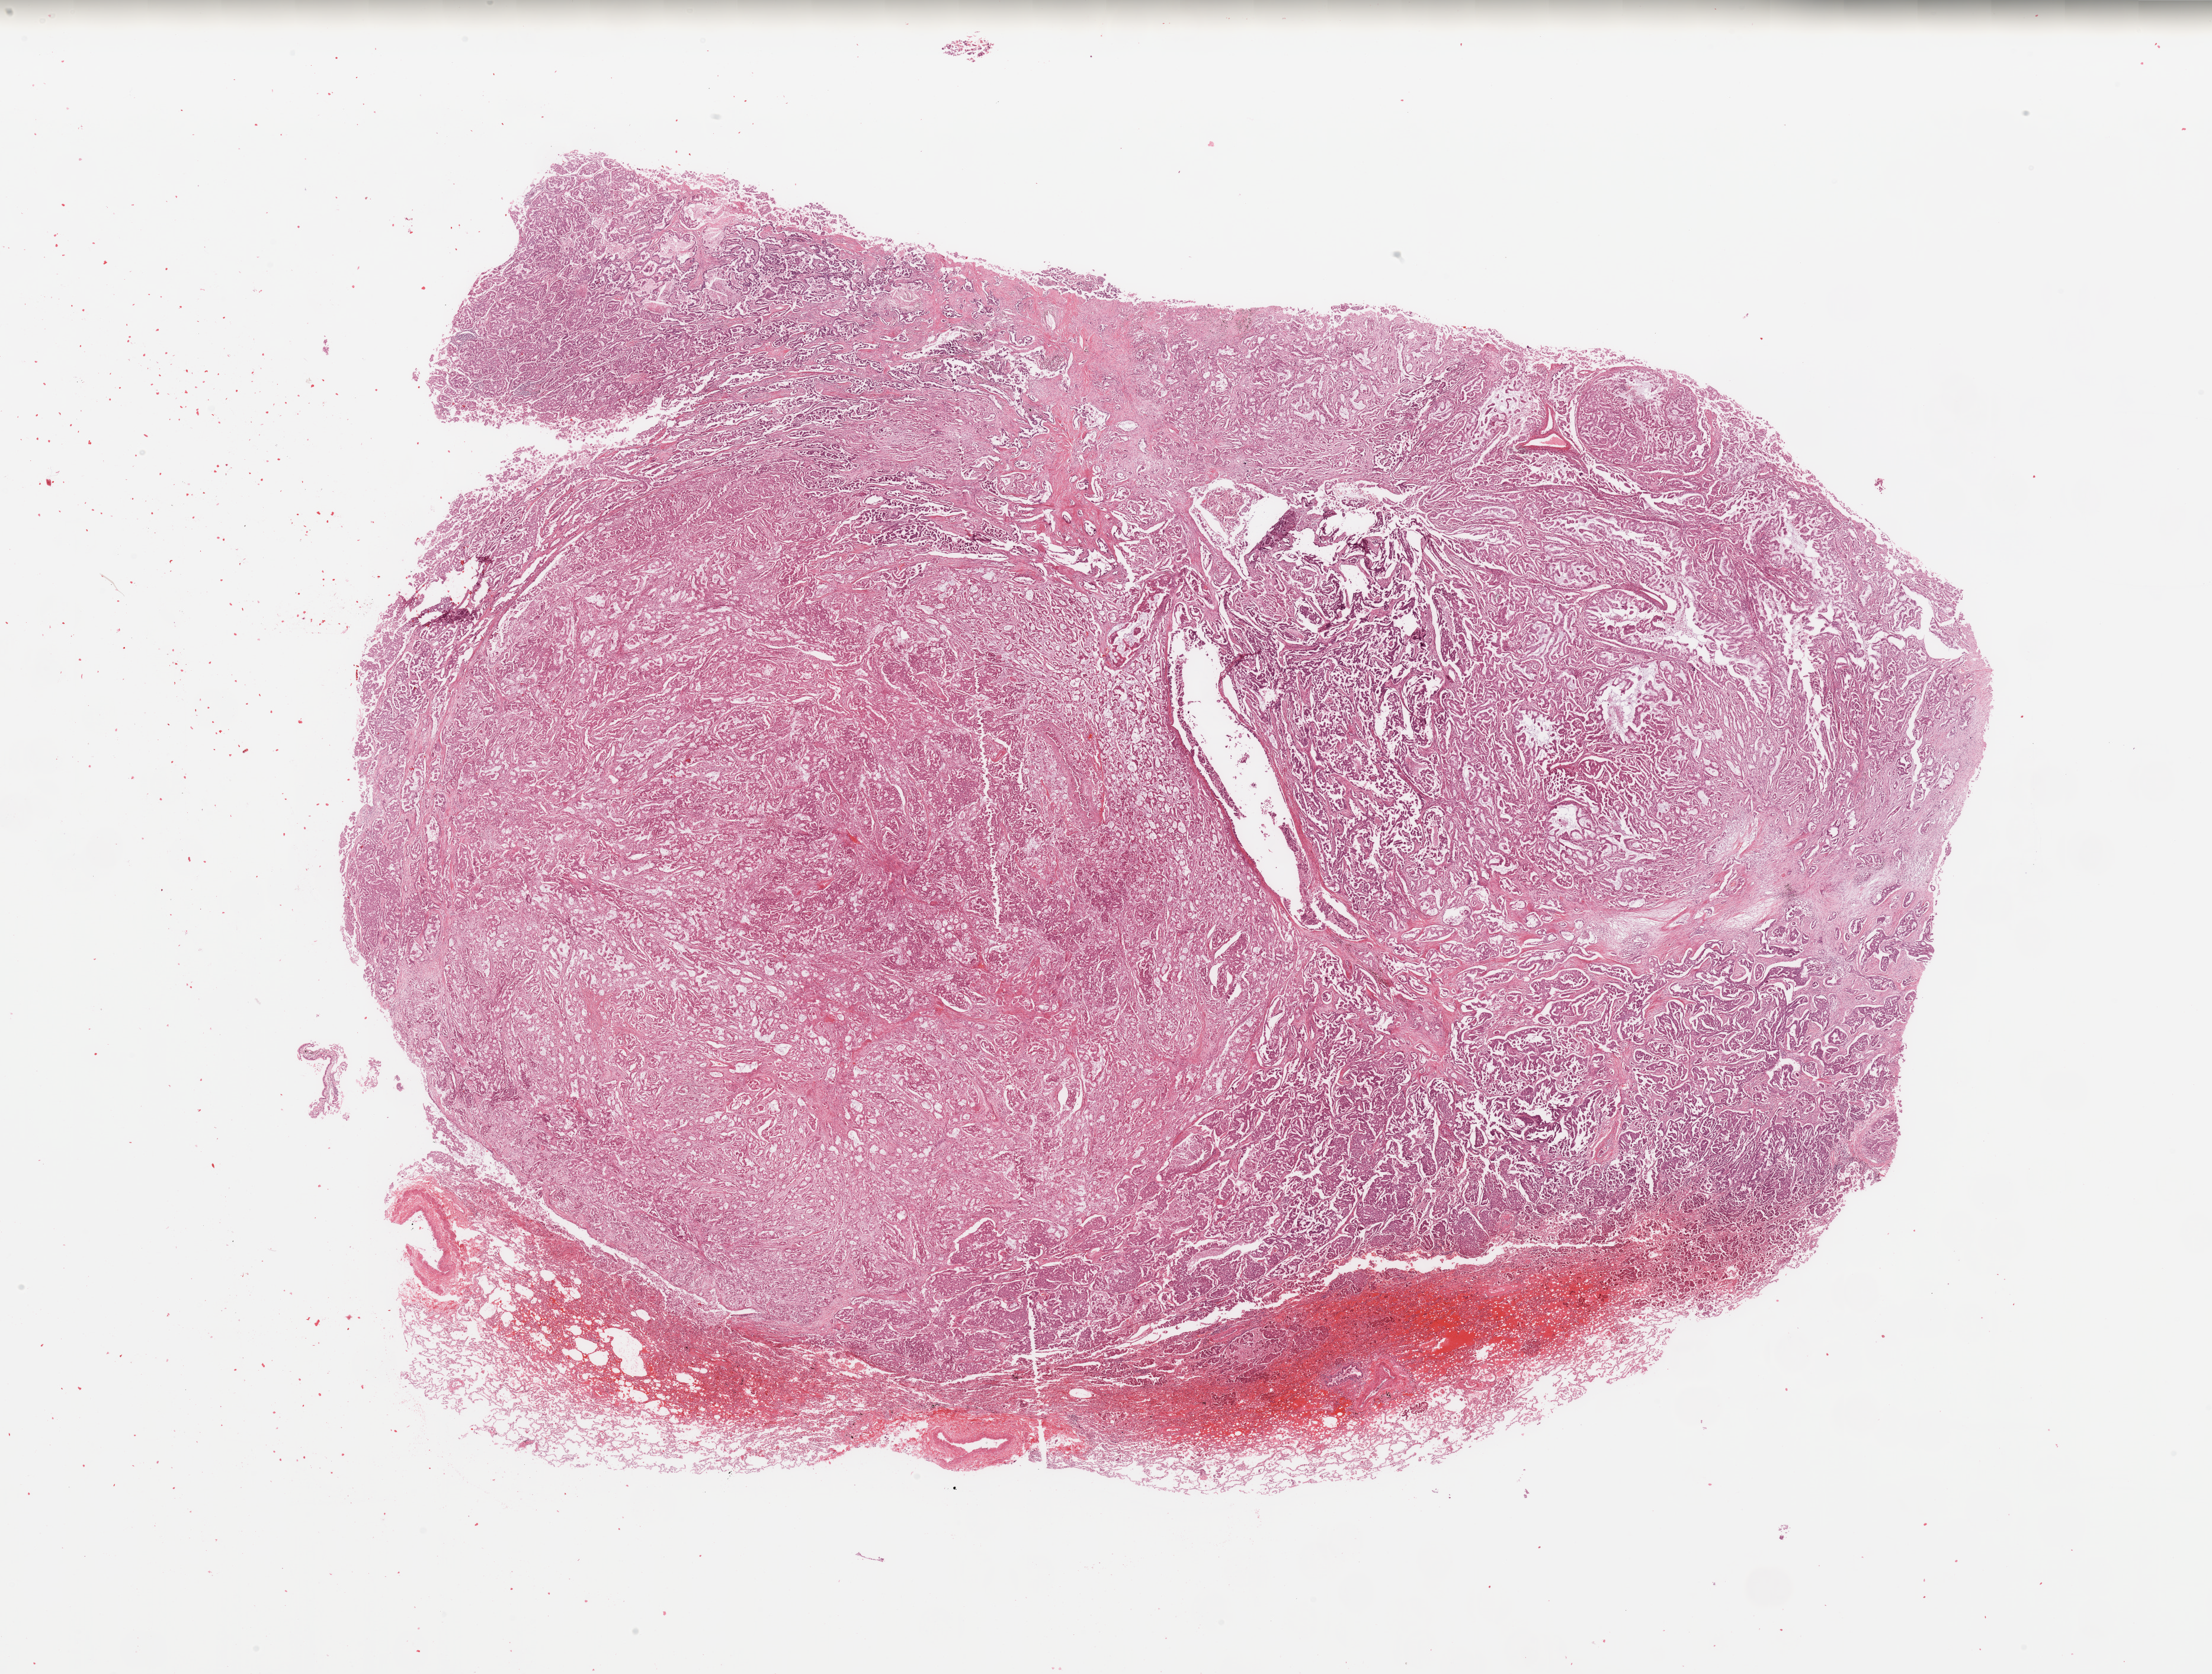
H&E whole-slide image, whole scanned area (about 29.5 x 22.3 mm, acquisition: 20x scan) shown as a low-resolution overview, tumour tissue sample, lung. Patient: male, age 55 years.
Diagnosis: Adenocarcinoma, NOS.